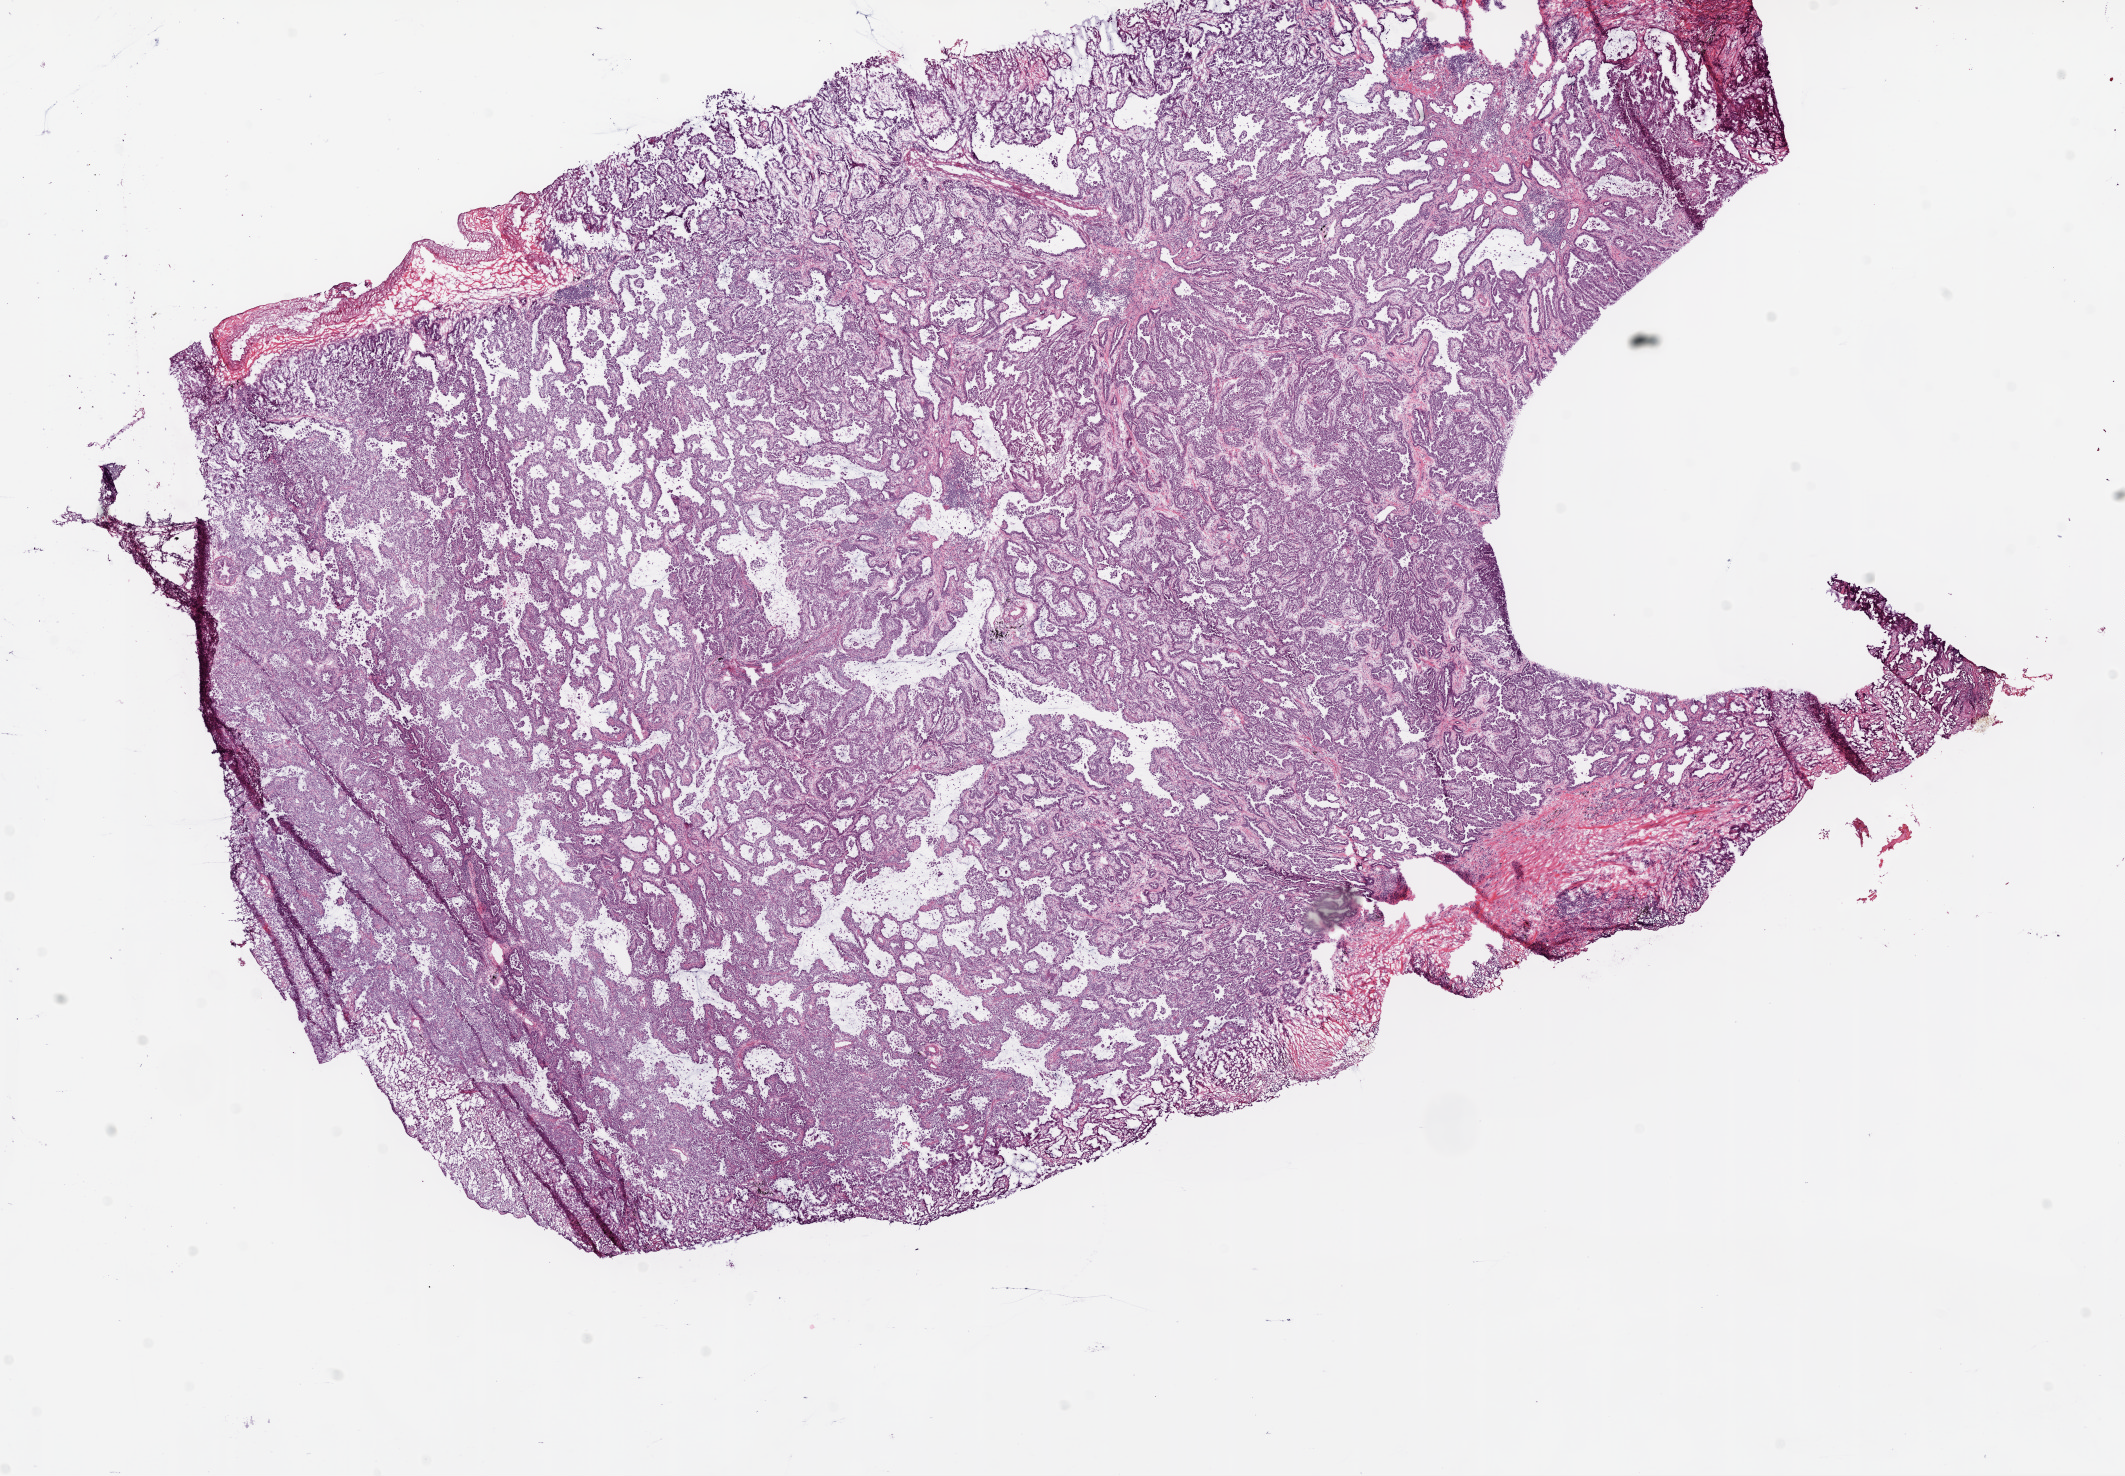
Digitized Hematoxylin and eosin (H&E) stained tissue section (whole slide), whole scanned area (about 17.1 x 11.8 mm) shown as a low-resolution overview, frozen section from the bottom of the tissue portion, sample: primary tumour, lung. Male patient; age at initial diagnosis 57 years. Pathologist review of this section (percent, as recorded): tumour cells 65%, tumour nuclei 80%, normal cells 0%, stromal cells 35%, necrosis 0%.
• AJCC pathologic stage: IB
• laterality: right
• histologic diagnosis: Adenocarcinoma, NOS